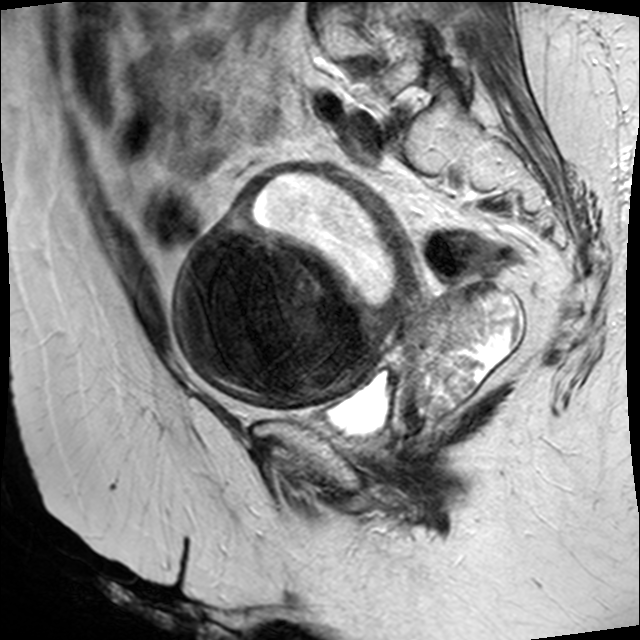
Pelvic MRI for cervical cancer, one sagittal slice; slice 19 of 45 in the series (ordered by position); T2-weighted; 1.5 T; TE 89 ms, TR 4610 ms; 4 mm slice thickness; 640 × 640 image matrix, field of view 260 × 260 mm. Female patient, age 50 years.
Outlined on this slice (expert manual segmentation):
- uterus and cervix: bounding box <173,162,522,438> (left, top, right, bottom; pixels)